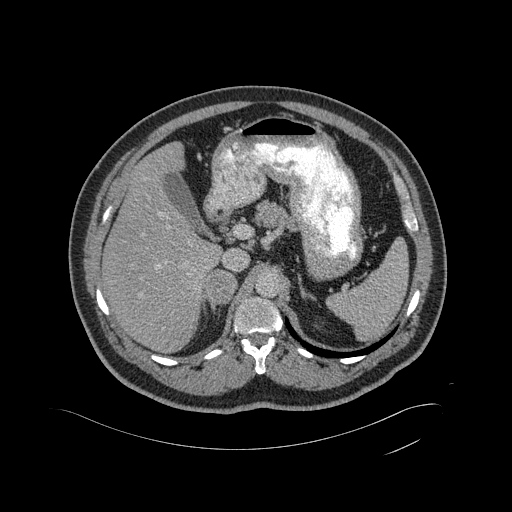
Contrast-enhanced abdominal CT, one axial slice; position 322 of 433 along the scan axis; 120 kVp; soft-tissue window (W 400 / L 40 HU); 2 mm slice thickness; 512 × 512 image matrix, field of view 500 × 500 mm. Patient: male, 56 years. From the clinical record (not read from this slice): diagnosis: adrenocortical carcinoma; tumour side: right adrenal; tumour size at pathology: 11.6 cm; Ki-67 index: 50 %; stage (as recorded): 3.
Annotated regions visible in this slice (semi-automatic segmentation, software-assisted and operator-edited):
- mass: box from (x=206, y=270) to (x=237, y=303) px